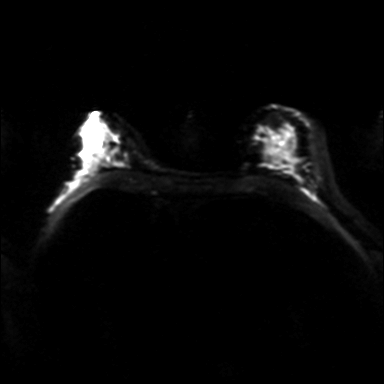
Breast MRI, one axial slice. Slice 23 of 36 in the series (ordered by position). Diffusion-weighted series; image 2 of 4 stored at this slice position (different b-values; order by instance number). 3 T. 4 mm slice thickness. 384 × 384 image matrix, field of view 320 × 320 mm. Female patient.
Structures marked on this image (outlined manually by an expert reader):
- tumour on diffusion-weighted imaging: bounding box <112,133,125,167> (left, top, right, bottom; pixels)